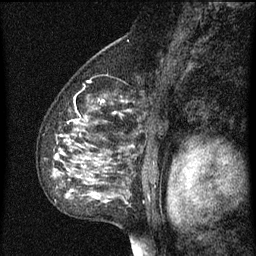
Breast MRI (dynamic contrast-enhanced), one sagittal slice. Position 47 of 60 along the scan axis. Dynamic contrast-enhanced series, image 2 of 3 at this slice position (ordered by acquisition). 1.5 T. TE 4.2 ms, TR 8 ms. 256 × 256 image matrix, field of view 180 × 180 mm. Female patient, age 55 years.
Outlined on this slice (semi-automatically segmented with operator editing):
- analysis volume of interest (the breast-tissue region the enhancement analysis was run in; not a lesion): box from (x=44, y=70) to (x=155, y=151) px
- tumour enhancement mask (voxels above the 70 % enhancement threshold inside the analysis volume of interest): (x=76, y=100)–(x=117, y=123)